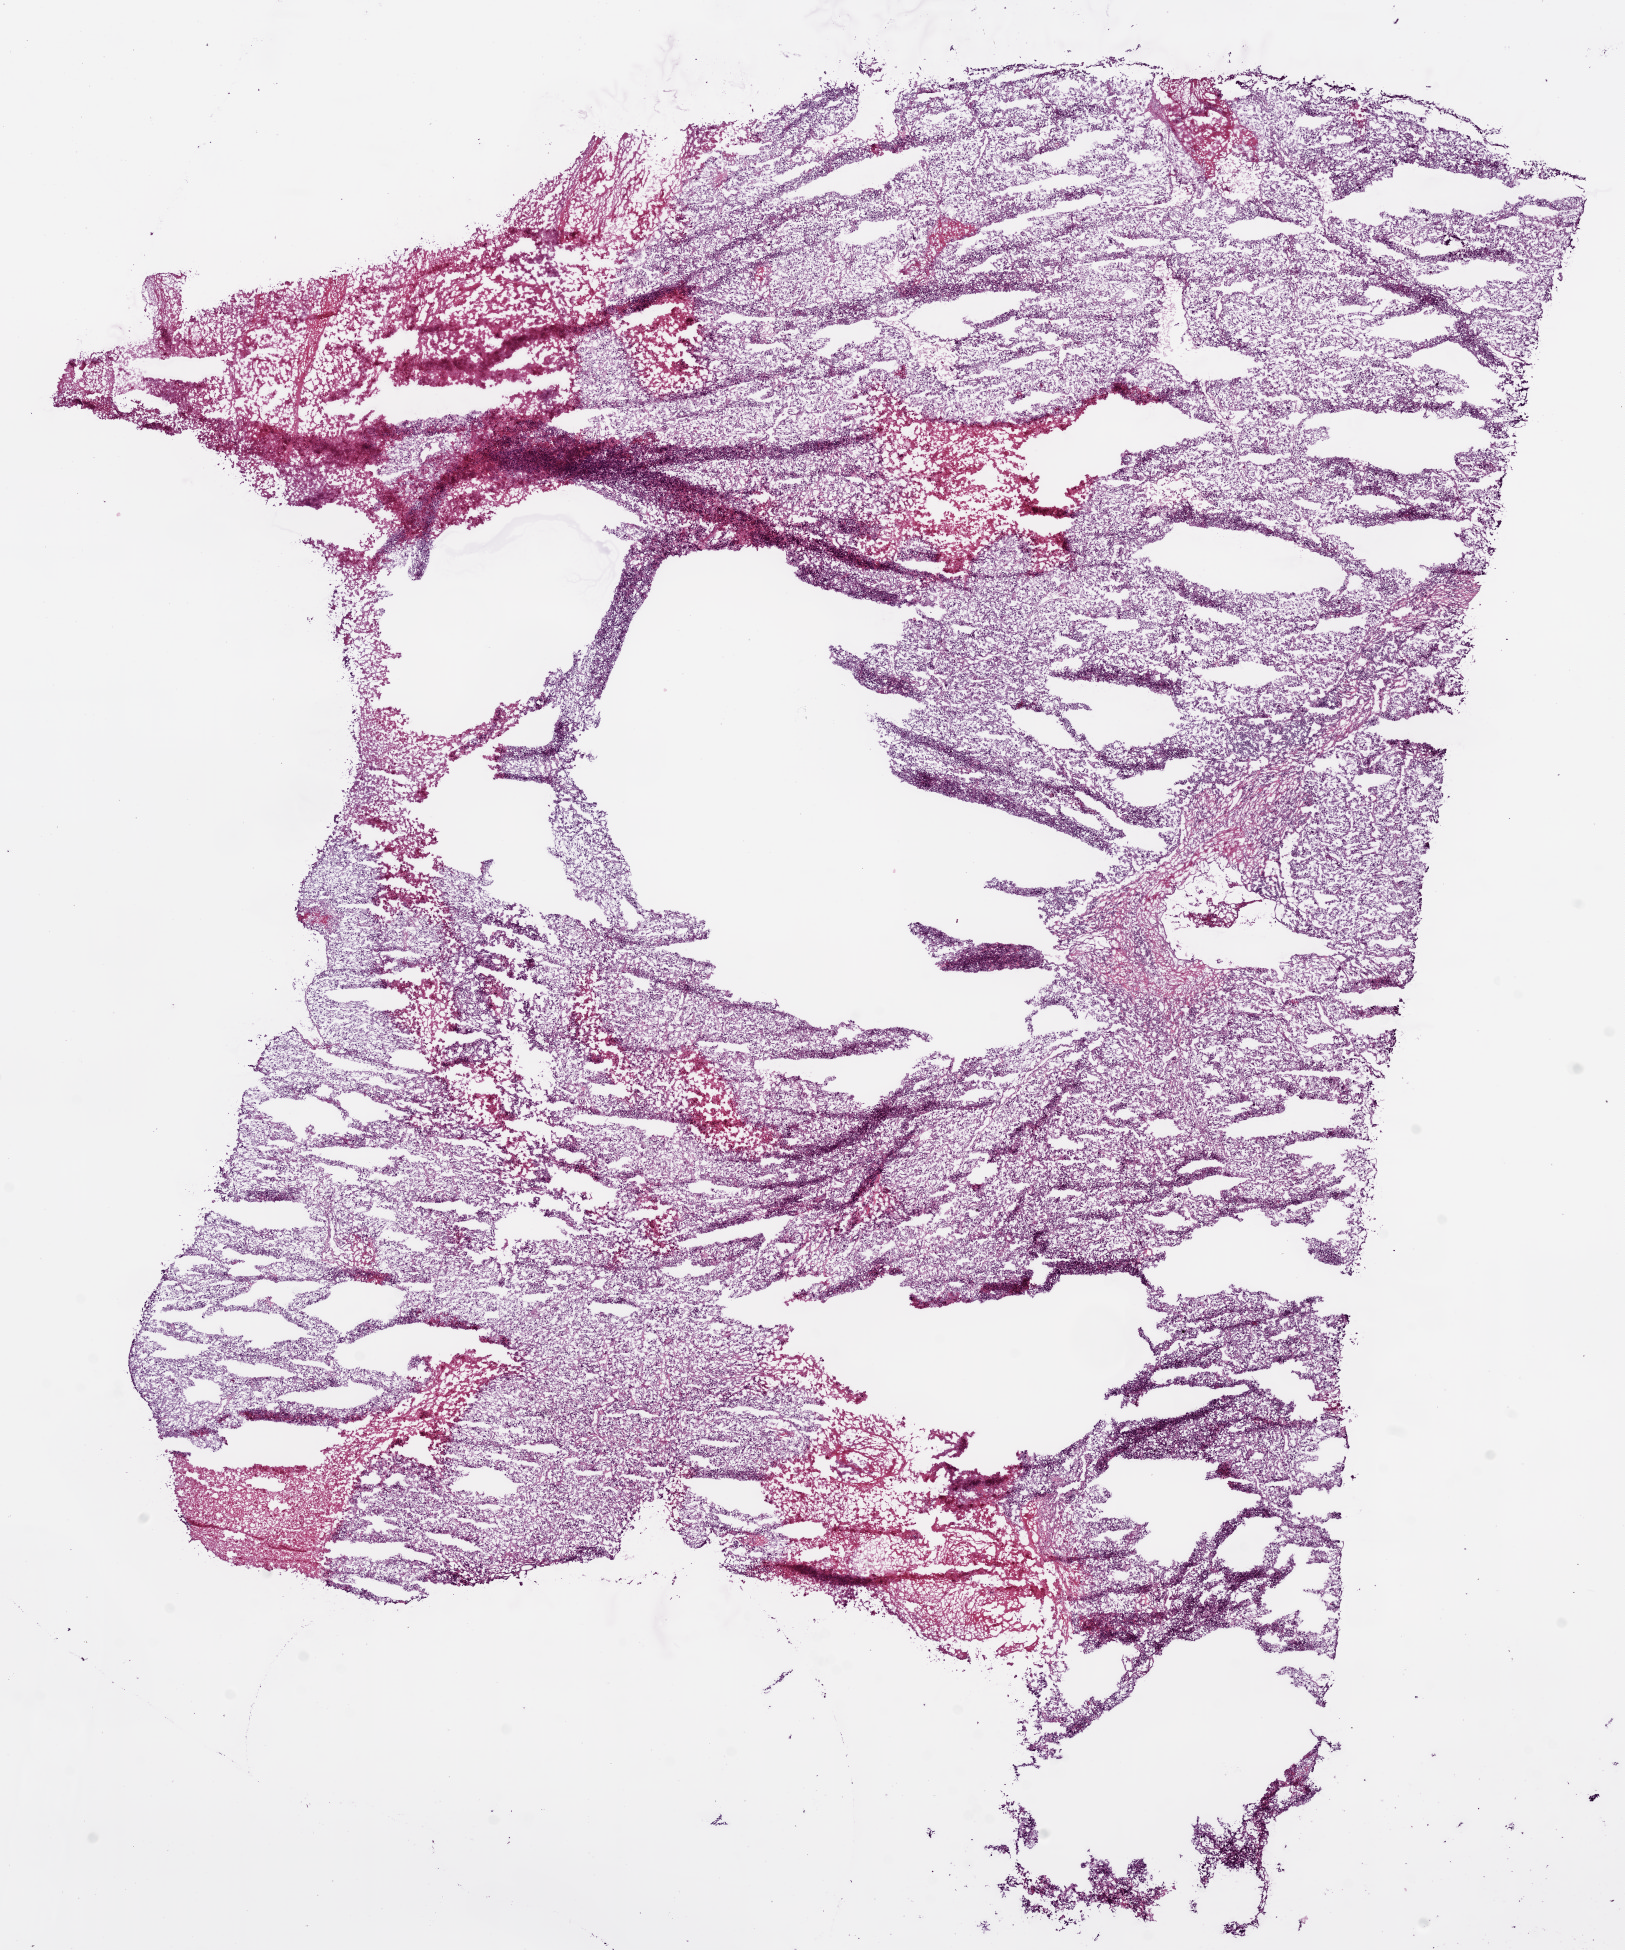
H&E whole-slide image, whole scanned area (about 13.0 x 15.6 mm, acquisition: 20x scan) shown as a low-resolution overview. Frozen section from the bottom of the tissue portion. Kidney, primary tumour sample. Male patient; age at initial diagnosis 39 years.
Diagnosis: Clear cell adenocarcinoma, NOS.